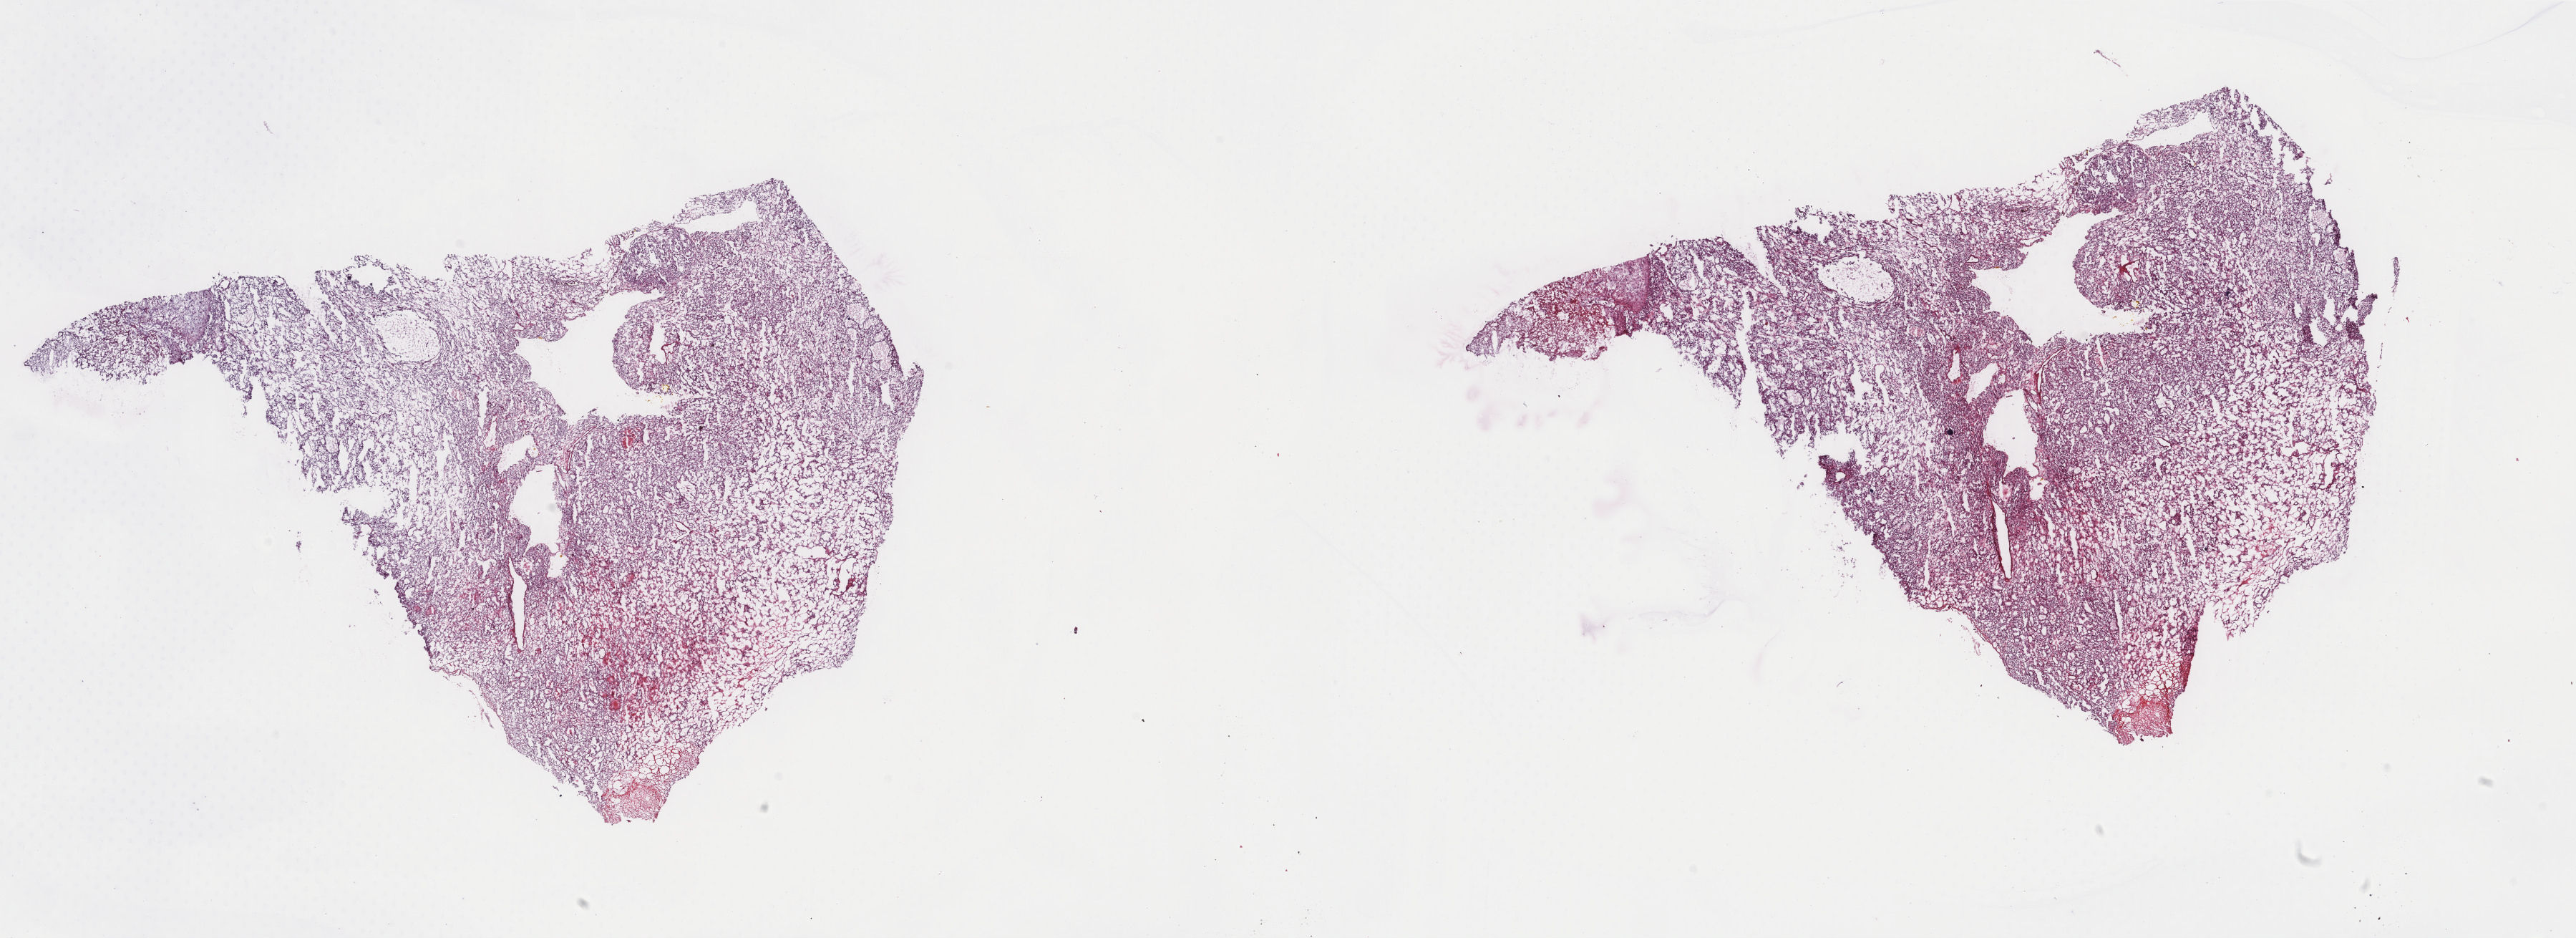
Hematoxylin and eosin (H&E) stained whole-slide image — a low-resolution overview of the entire scanned area, about 28.6 x 10.4 mm; frozen section from the top of the tissue portion; kidney, primary tumour sample. Female patient; age at initial diagnosis 72 years. Histologic grade: G2 (moderately differentiated). Slide review estimates, as recorded: tumour cells 100%, tumour nuclei 80%, normal cells 0%, stromal cells 0%, necrosis 0%. Infiltration values recorded for this section: lymphocyte infiltration 1%, monocyte infiltration 1%, neutrophil infiltration 0%.
AJCC pathologic stage: I (7th edition). Laterality: right. Histologic diagnosis: Renal cell carcinoma, NOS. TNM: T1a NX MX.